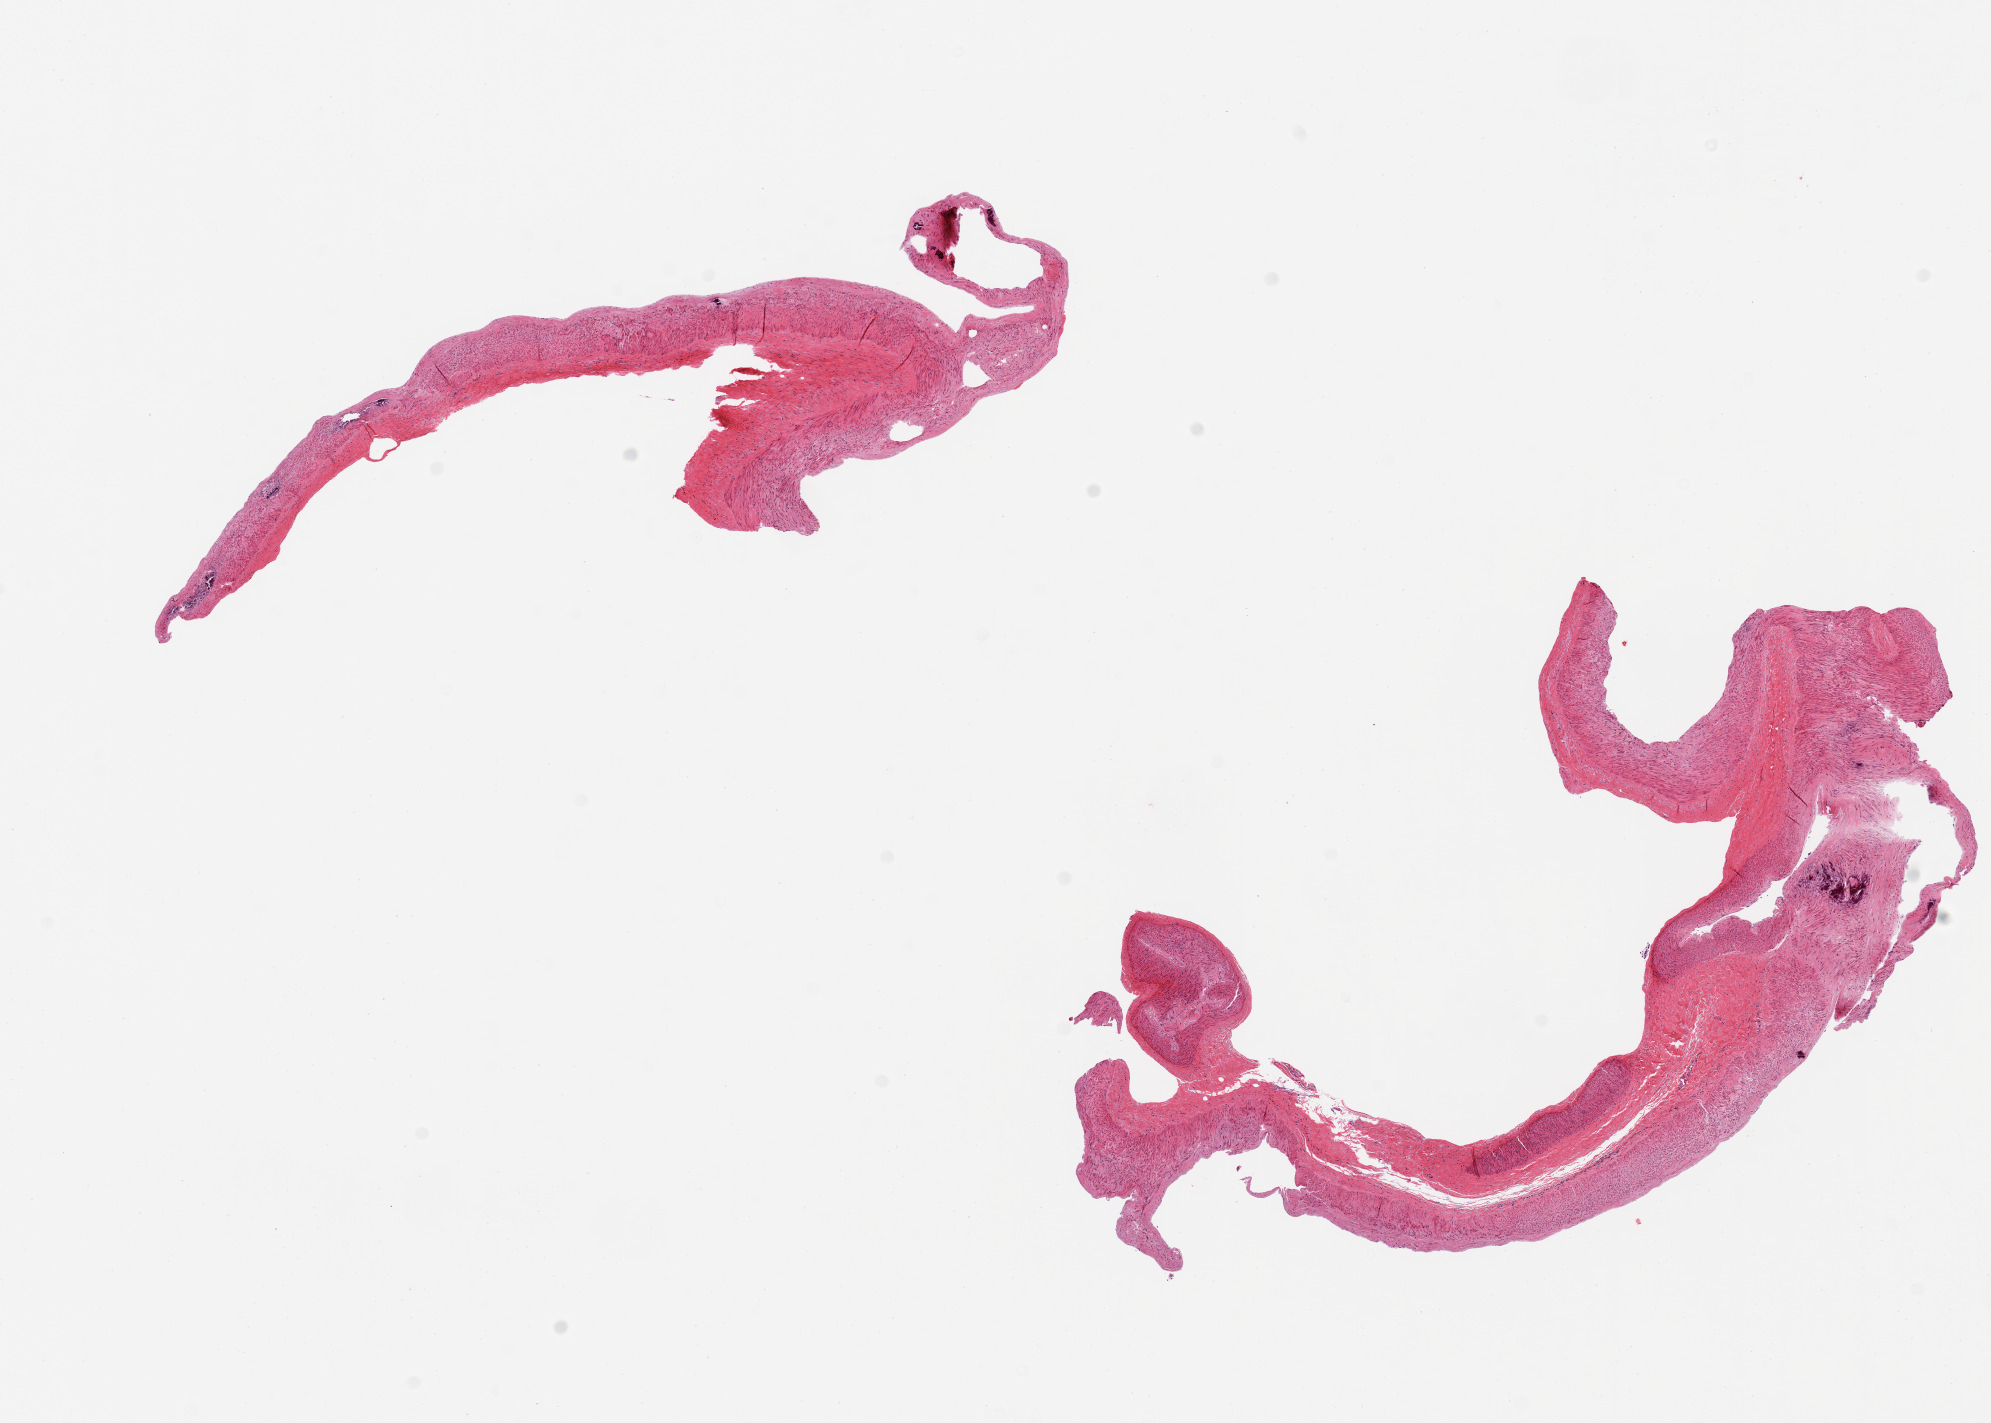
Hematoxylin and eosin (H&E) whole-slide image, a low-resolution overview of the entire scanned area, about 15.8 x 11.3 mm. PAXgene-fixed paraffin-embedded (PFPE) section. Target tissue: tibial artery. Donor tissue sample.
Pathologist's review note for this sample: 2 pieces, disrupted portions of artery, medial calcification.